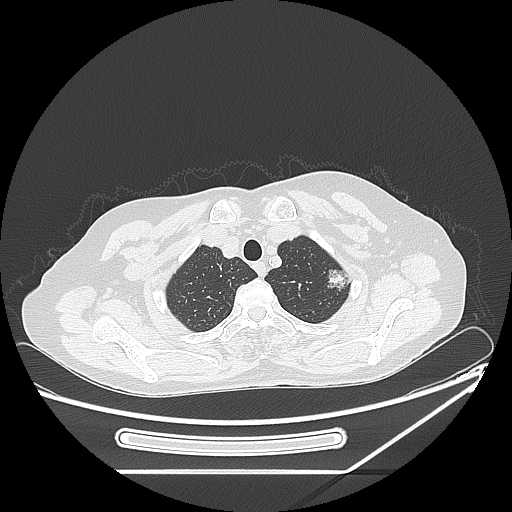
Chest CT, one axial slice. 120 kVp. Lung window (W 1500 / L -600 HU). 512 × 512 image matrix, field of view 409 × 409 mm. Patient: female, 57 years. From the clinical record (not read from this slice): clinical TNM (as recorded): T1c N0 M0; histopathological grade: G2-3.
Annotated regions visible in this slice (rectangle marked by the reading radiologist):
- lung tumour (recorded histology: adenocarcinoma): bounding box (x1, y1, x2, y2) in pixels: (325, 265, 354, 292)